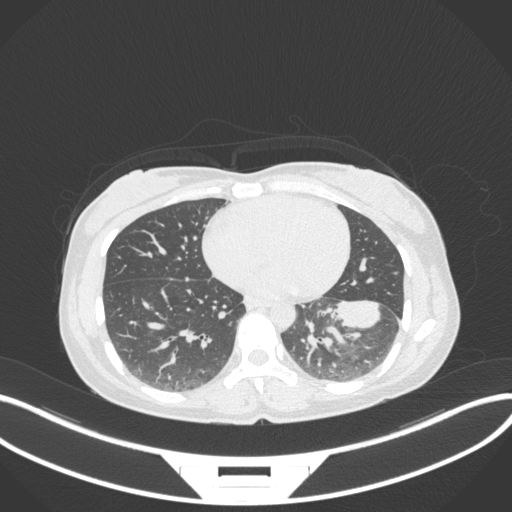
Chest CT, one axial slice; position 141 of 361 along the scan axis; reconstruction kernel B31f; 120 kVp; lung window (W 1500 / L -600 HU); 512 × 512 image matrix, field of view 400 × 400 mm. Female patient, age 41 years. Case-level facts recorded for this patient, not image findings: clinical TNM (as recorded): T2a N3 M1b.
Annotated regions visible in this slice (rectangle marked by the reading radiologist):
- lung tumour (recorded histology: adenocarcinoma): box from (x=328, y=294) to (x=389, y=333) px